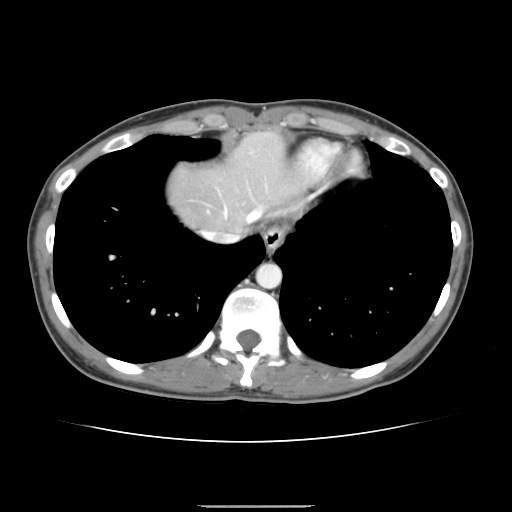
Contrast-enhanced abdominal CT, one axial slice. Position 132 of 150 along the scan axis. 120 kVp. Intravenous contrast given. Soft-tissue window (W 400 / L 40 HU). 2.5 mm slice thickness. 512 × 512 image matrix. Female patient, age 32 years. From the clinical record (not read from this slice): diagnosis: colorectal cancer liver metastases, imaged before liver resection; multiple liver metastases: yes.
Outlined on this slice (manually delineated by an expert):
- hepatic veins: bounding box (x1, y1, x2, y2) in pixels: (202, 207, 262, 242)
- liver: (169, 132, 307, 231)
- planned liver remnant (the part of the liver to remain after resection): (169, 132, 307, 232)